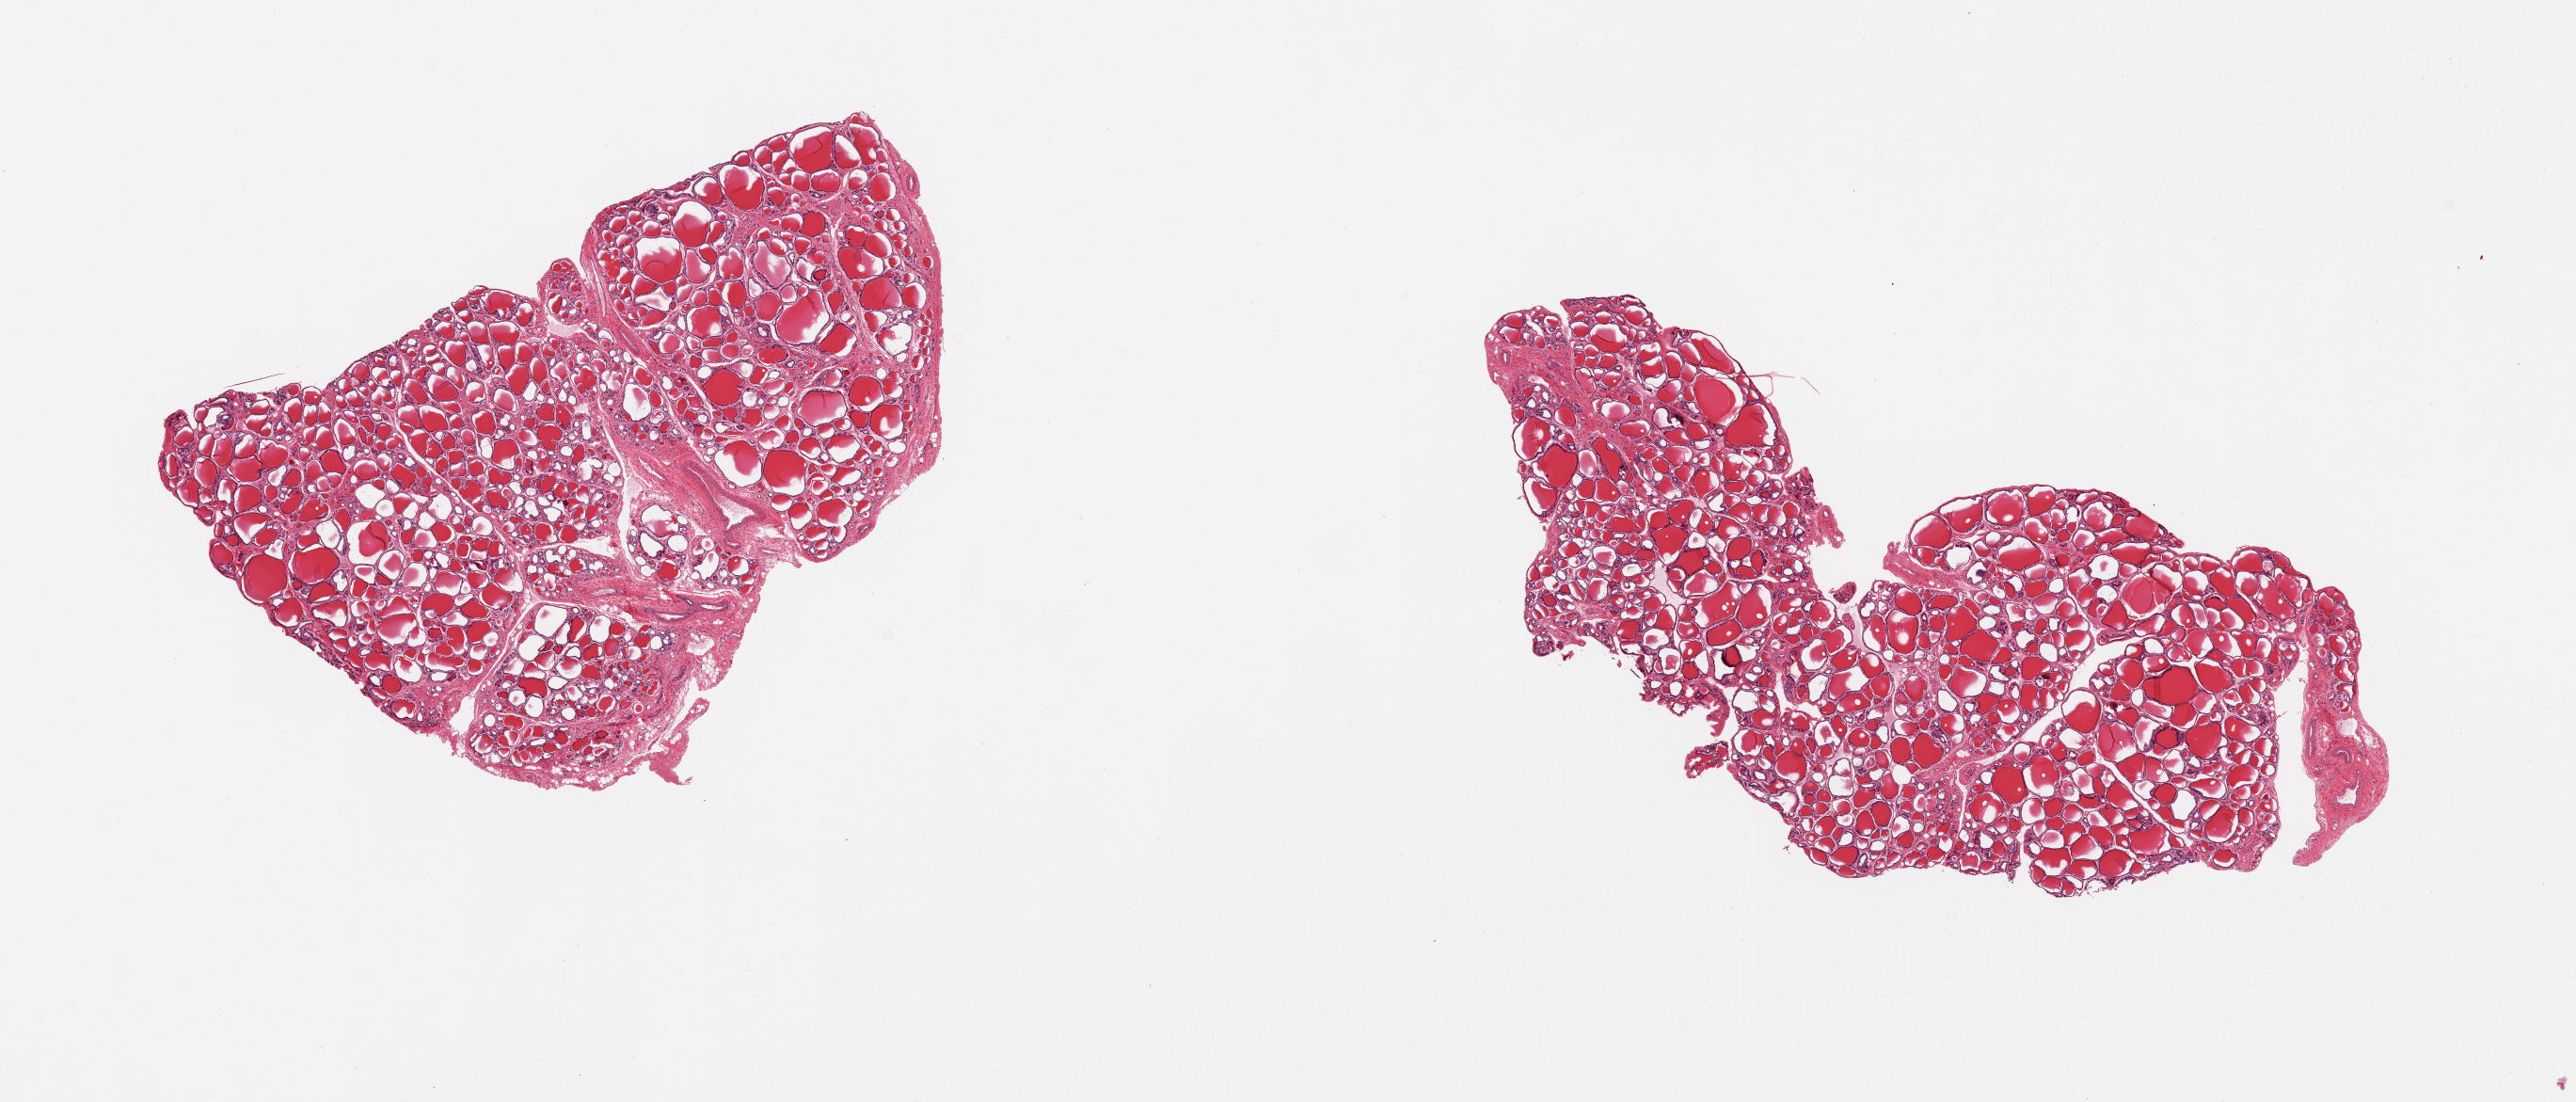
H&E whole-slide image, brightfield — low-resolution overview of the scanned area, about 21.7 x 9.3 mm (acquisition: 20x scan). PAXgene-fixed, paraffin-embedded tissue. Section of thyroid (target tissue). Donor tissue sample. Donor sex: male.
Reviewer comment on this tissue sample: 2 pieces, no abnormalities.